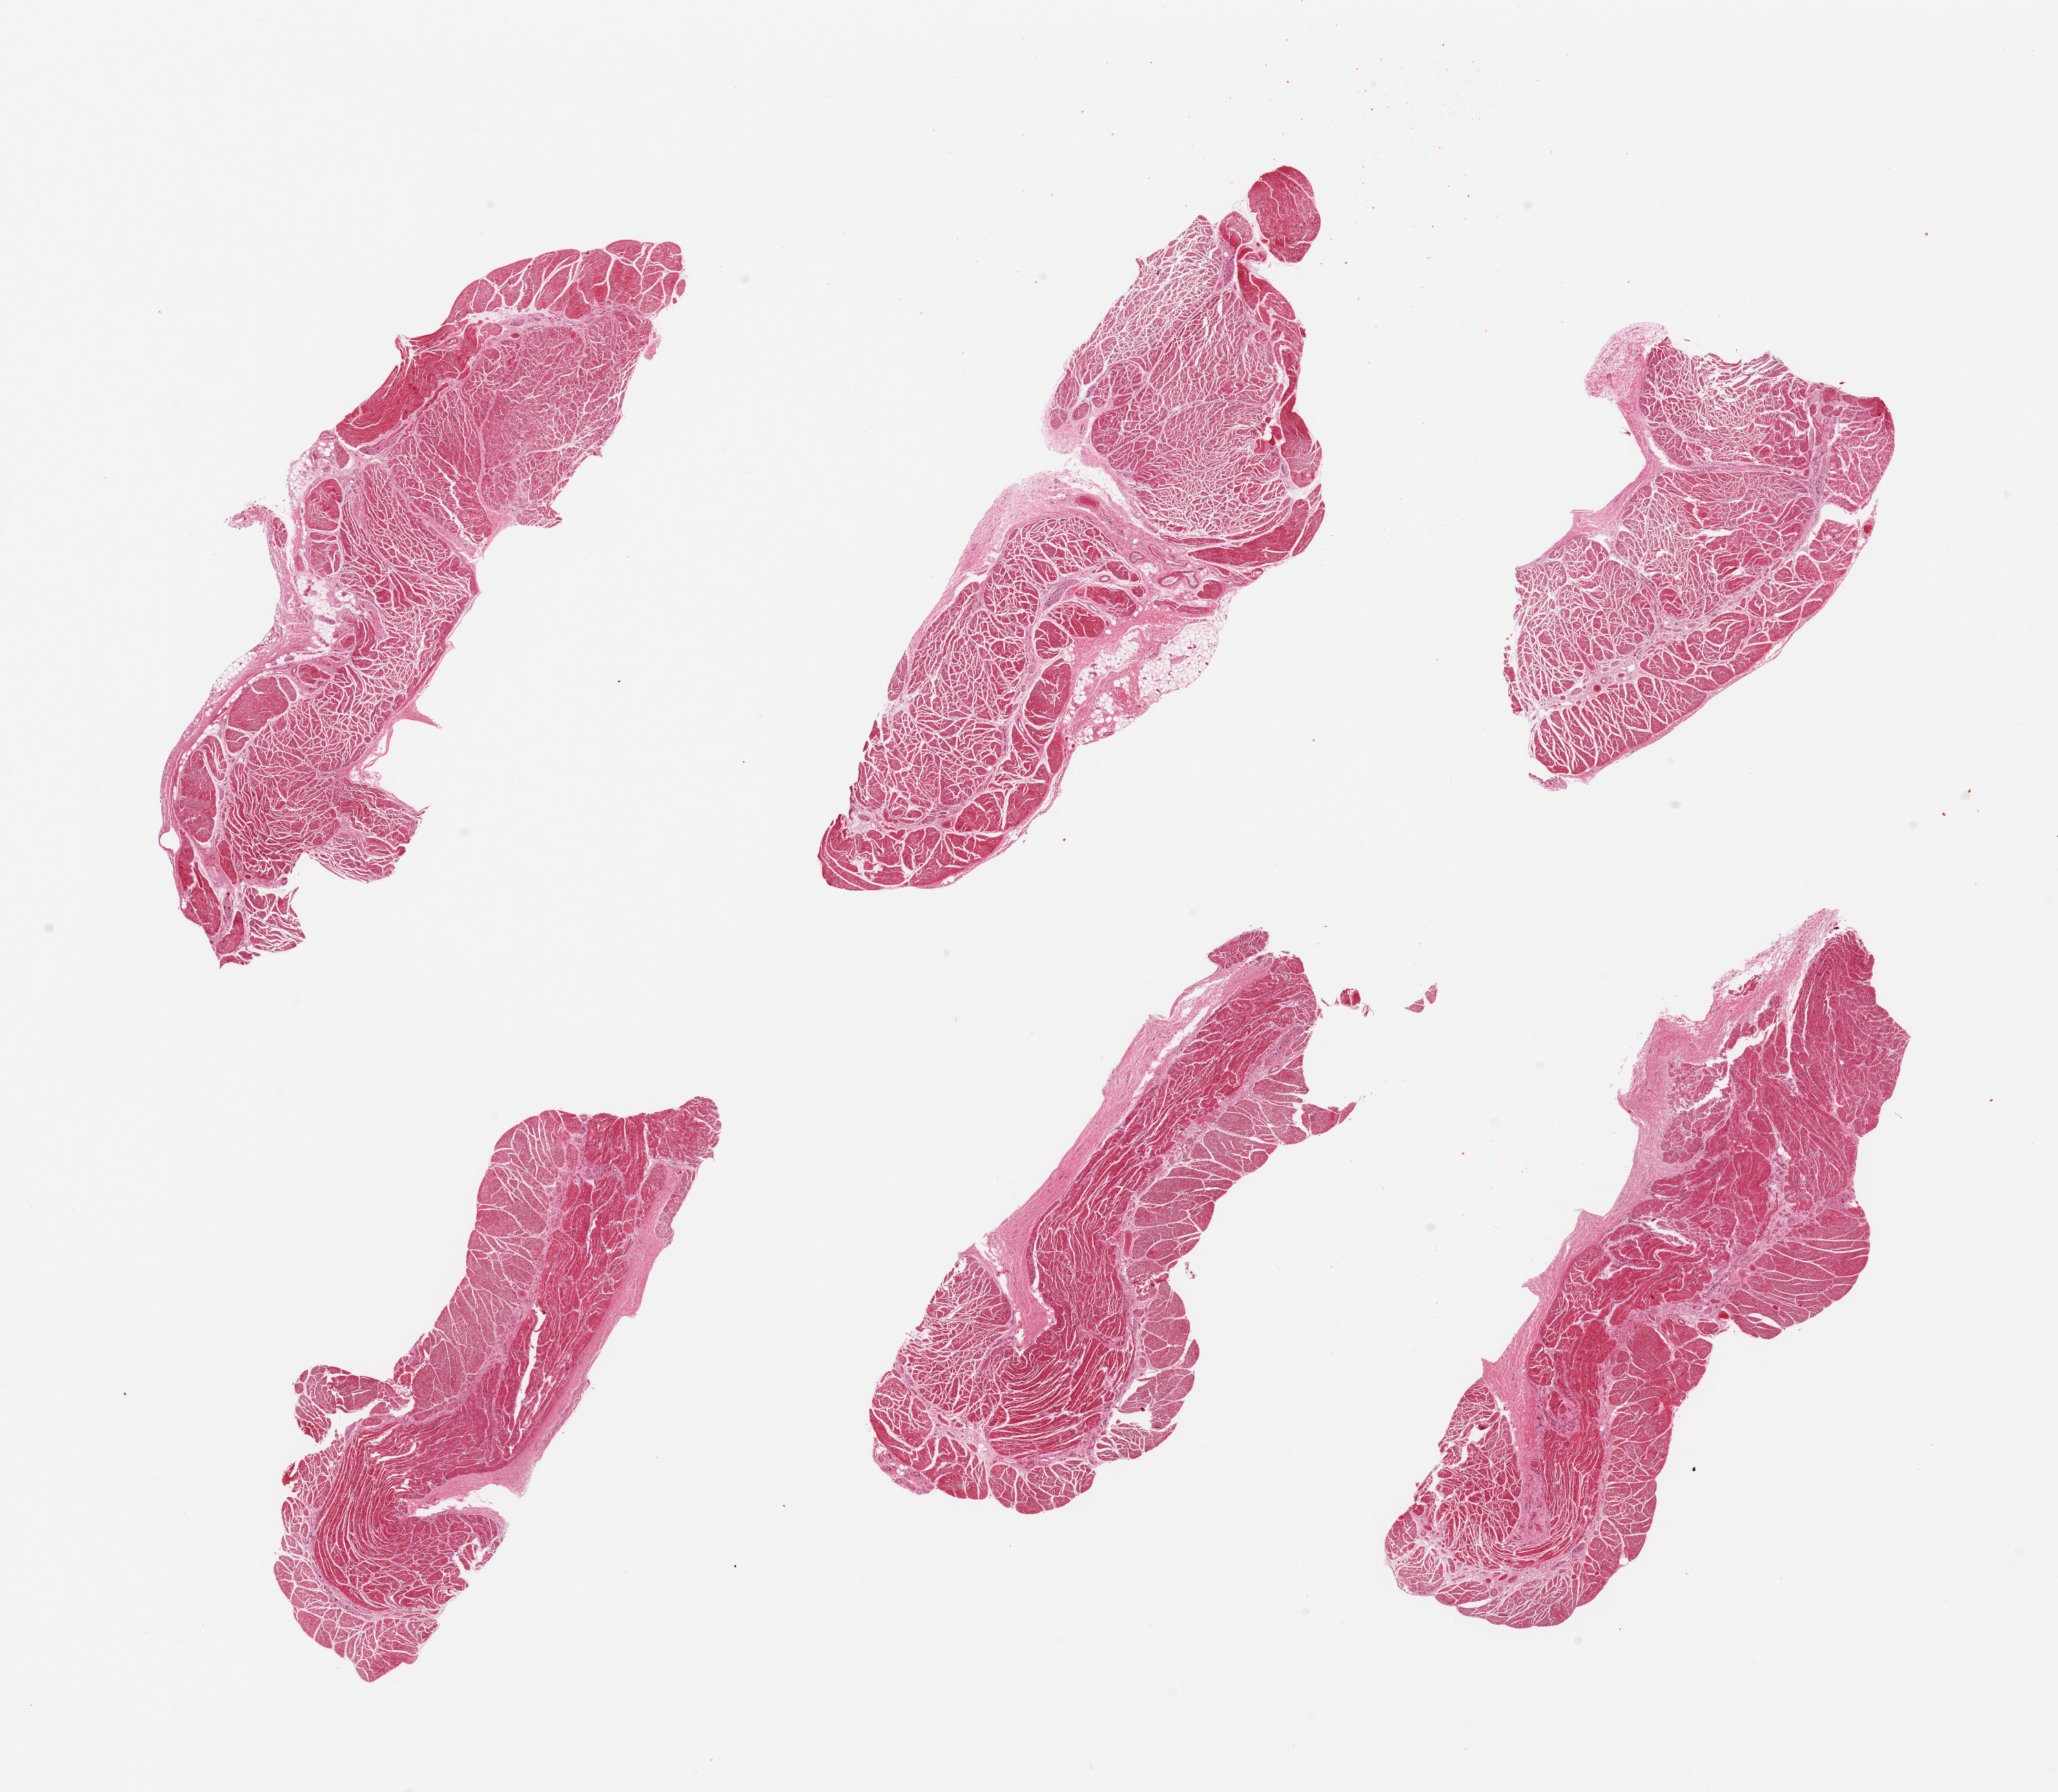
Digitized haematoxylin and eosin-stained section, brightfield — whole scanned area (about 23.6 x 20.6 mm) shown as a low-resolution overview. PAXgene-fixed paraffin-embedded (PFPE) section. Sampled site (target tissue): esophageal muscle. Donor tissue sample. Female donor.
Reviewer comment on this tissue sample: 6 pieces; target muscularis.